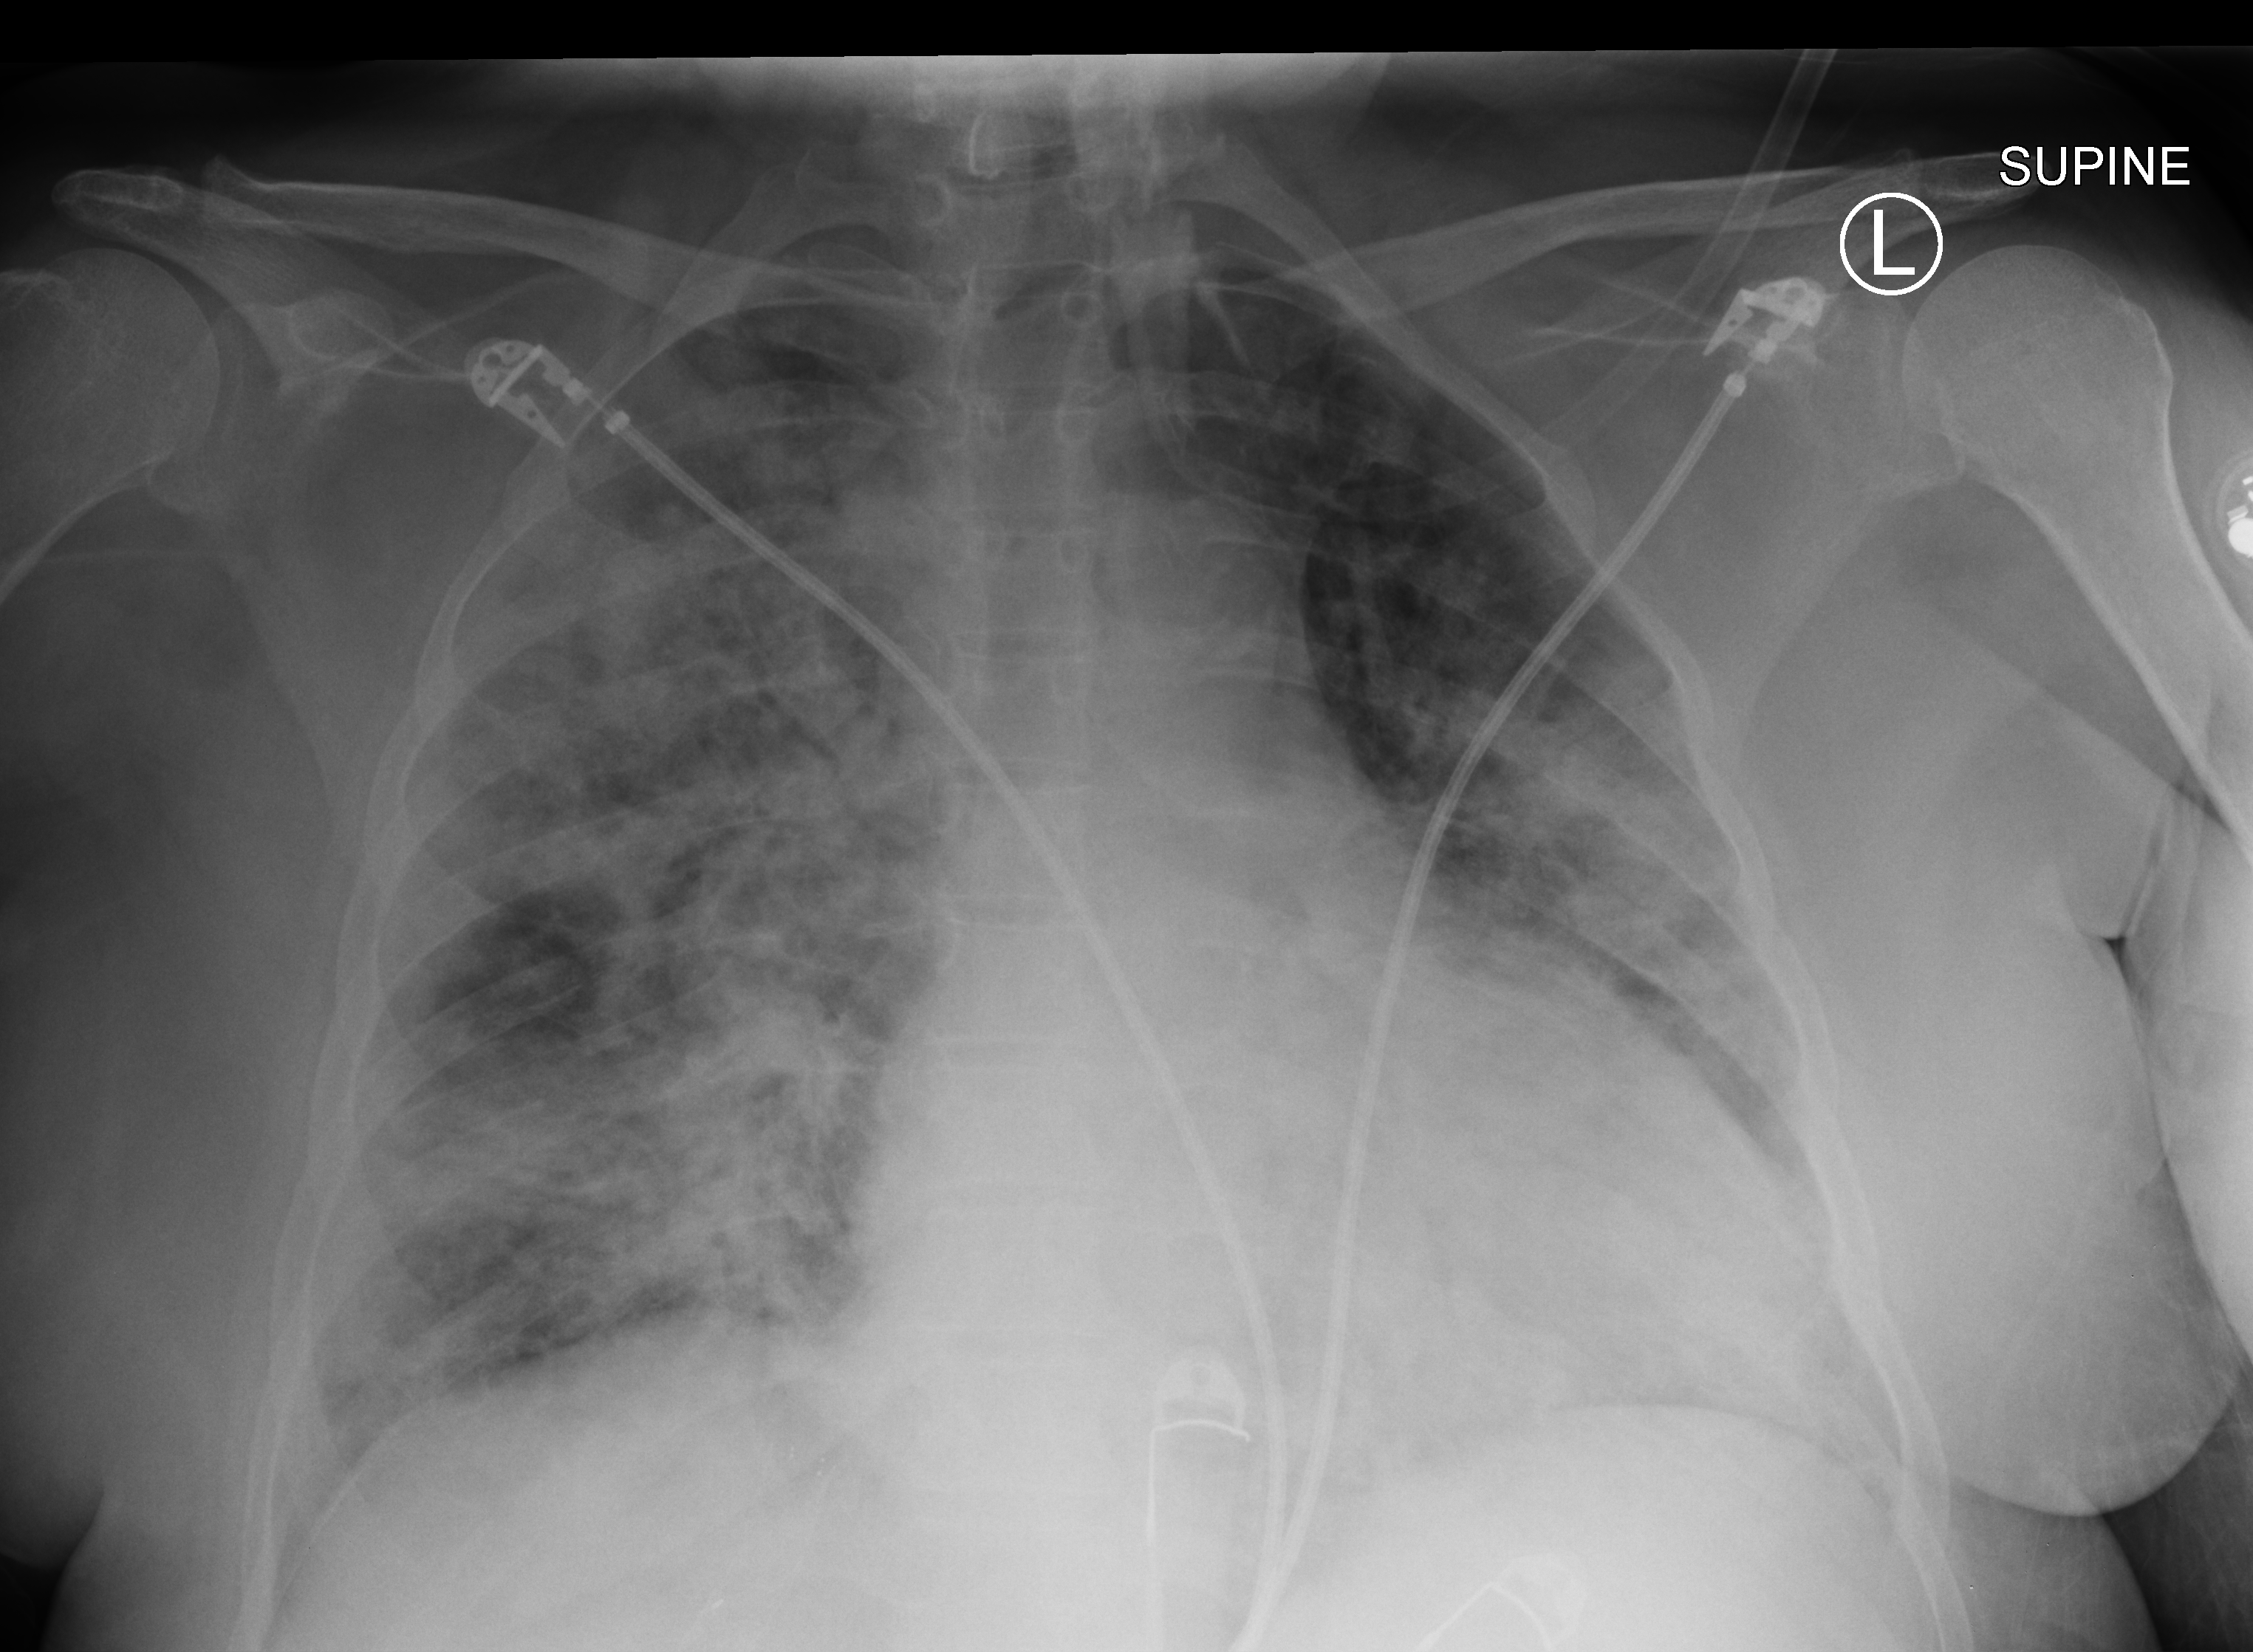
Bedside chest radiograph (computed radiography), anteroposterior (AP) projection. Patient hospitalised with COVID-19; female, aged 60–74 years.
From the hospital-stay record, not from the radiograph (when in the stay this image was taken is not recorded): mechanically ventilated during this hospital stay: no; diabetes (admission record): yes; admitted to intensive care during this hospital stay: yes.